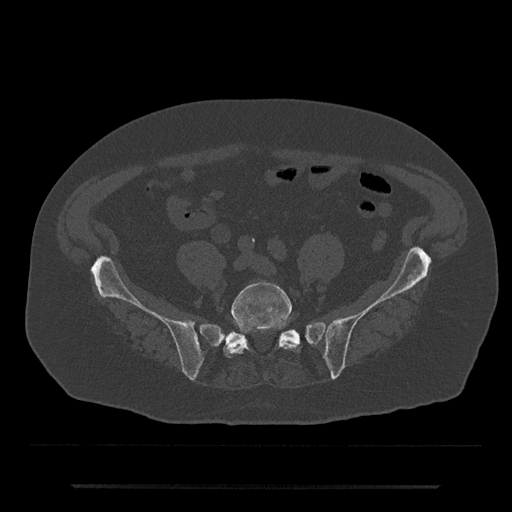
CT including the spine, one axial slice; bone window (W 1800 / L 400 HU); 0.5 mm slice thickness; 512 × 512 image matrix. Male patient, age 80 years. Case-level facts recorded for this patient, not image findings: primary cancer: prostate; vertebrae with lytic lesions (as recorded): L1, T11.
Structures marked on this image (semi-automatically segmented with operator editing):
- L5 vertebra: bounding box <223,281,299,357> (left, top, right, bottom; pixels)